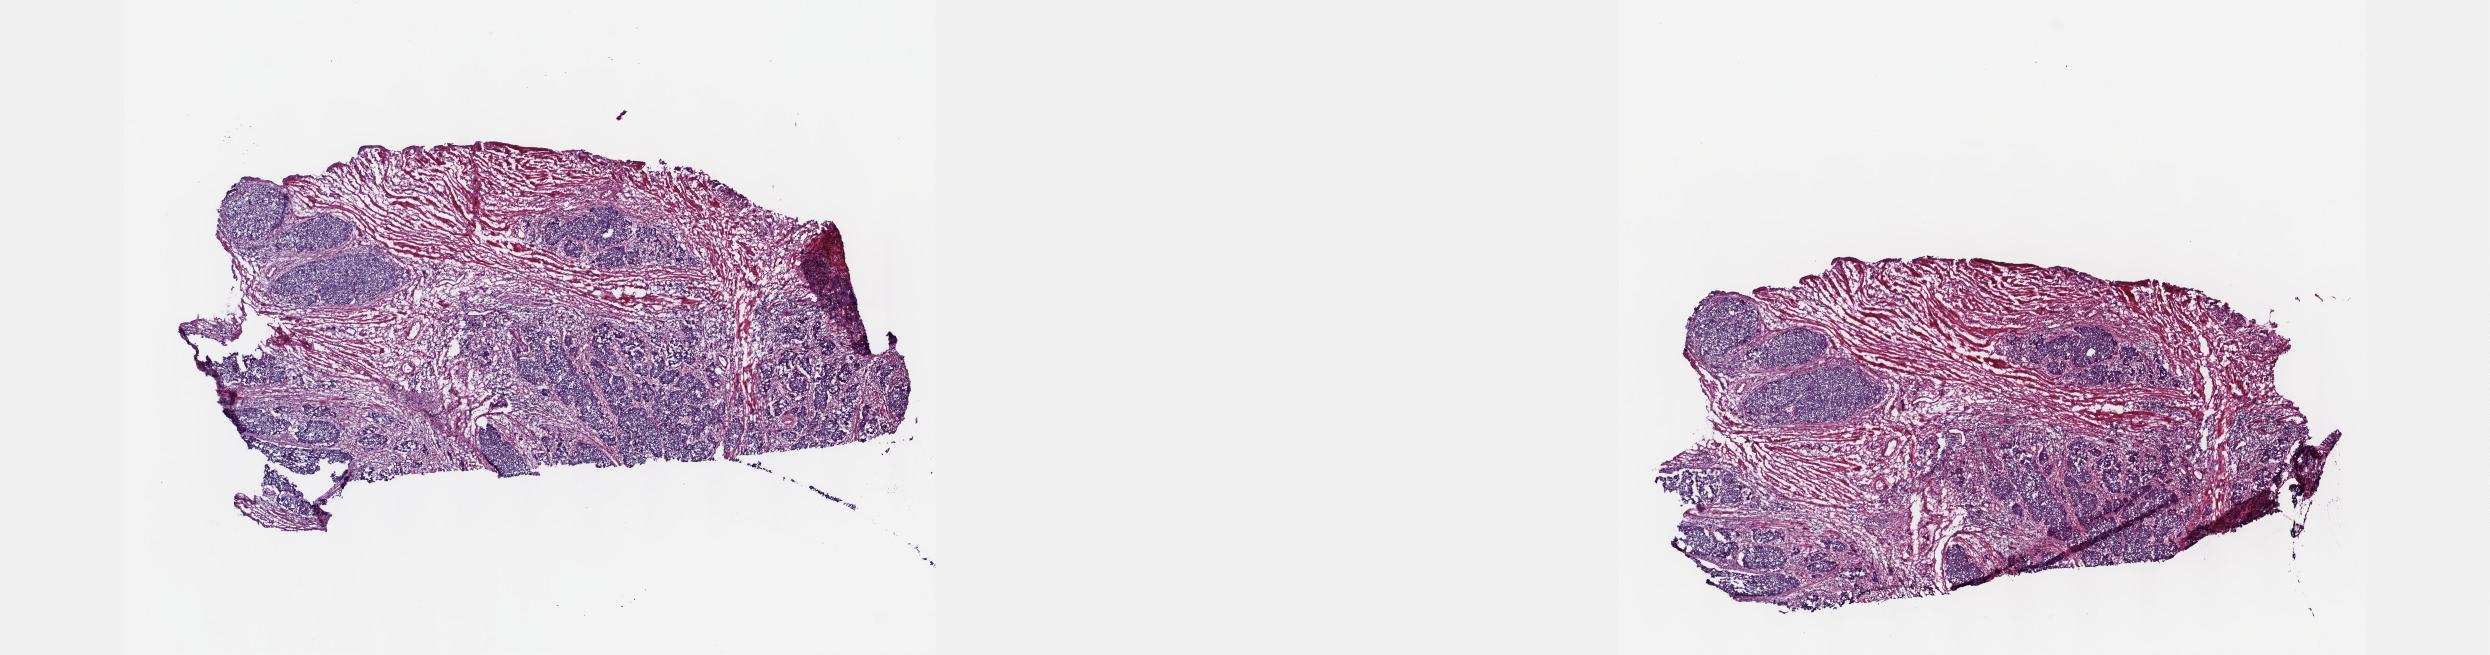
Digitized Hematoxylin and eosin (H&E) stained tissue section (whole slide) — a low-resolution overview of the entire scanned area, about 20.1 x 5.3 mm. Frozen section from the top of the tissue portion. Sample: primary tumour, esophagus. Male, age 62 years at initial diagnosis. Histologic grade: G3 (poorly differentiated). Slide review estimates, as recorded: tumour cells 30%, tumour nuclei 80%, normal cells 0%, stromal cells 70%, necrosis 0%. Infiltration values recorded for this section: lymphocyte infiltration 8%, monocyte infiltration 12%, neutrophil infiltration 0%.
AJCC pathologic stage: IIIB (7th edition). Histologic diagnosis: Squamous cell carcinoma, NOS (lower third of esophagus). Lymph nodes positive (case pathology): 6 of 20 examined.